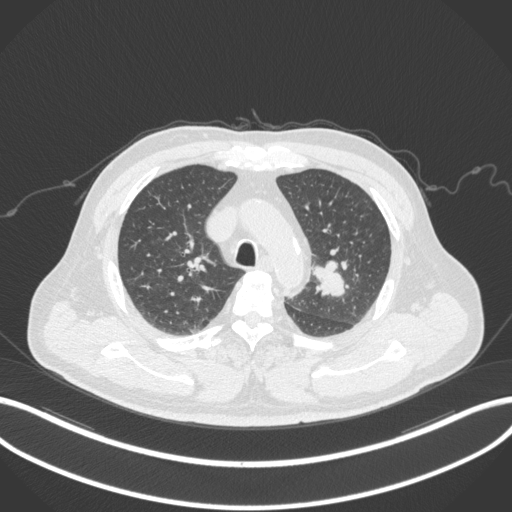
Chest CT, one axial slice. Position 225 of 286 along the scan axis. Reconstruction kernel B31f. 120 kVp. Lung window (W 1500 / L -600 HU). 512 × 512 image matrix, field of view 400 × 400 mm. Patient: male, 67 years. From the clinical record (not read from this slice): clinical TNM (as recorded): T2a N1 M0; histopathological grade: G3.
Structures marked on this image (rectangle marked by the reading radiologist):
- lung tumour (recorded histology: adenocarcinoma): bounding box [x1, y1, x2, y2] px = [313, 255, 351, 301]